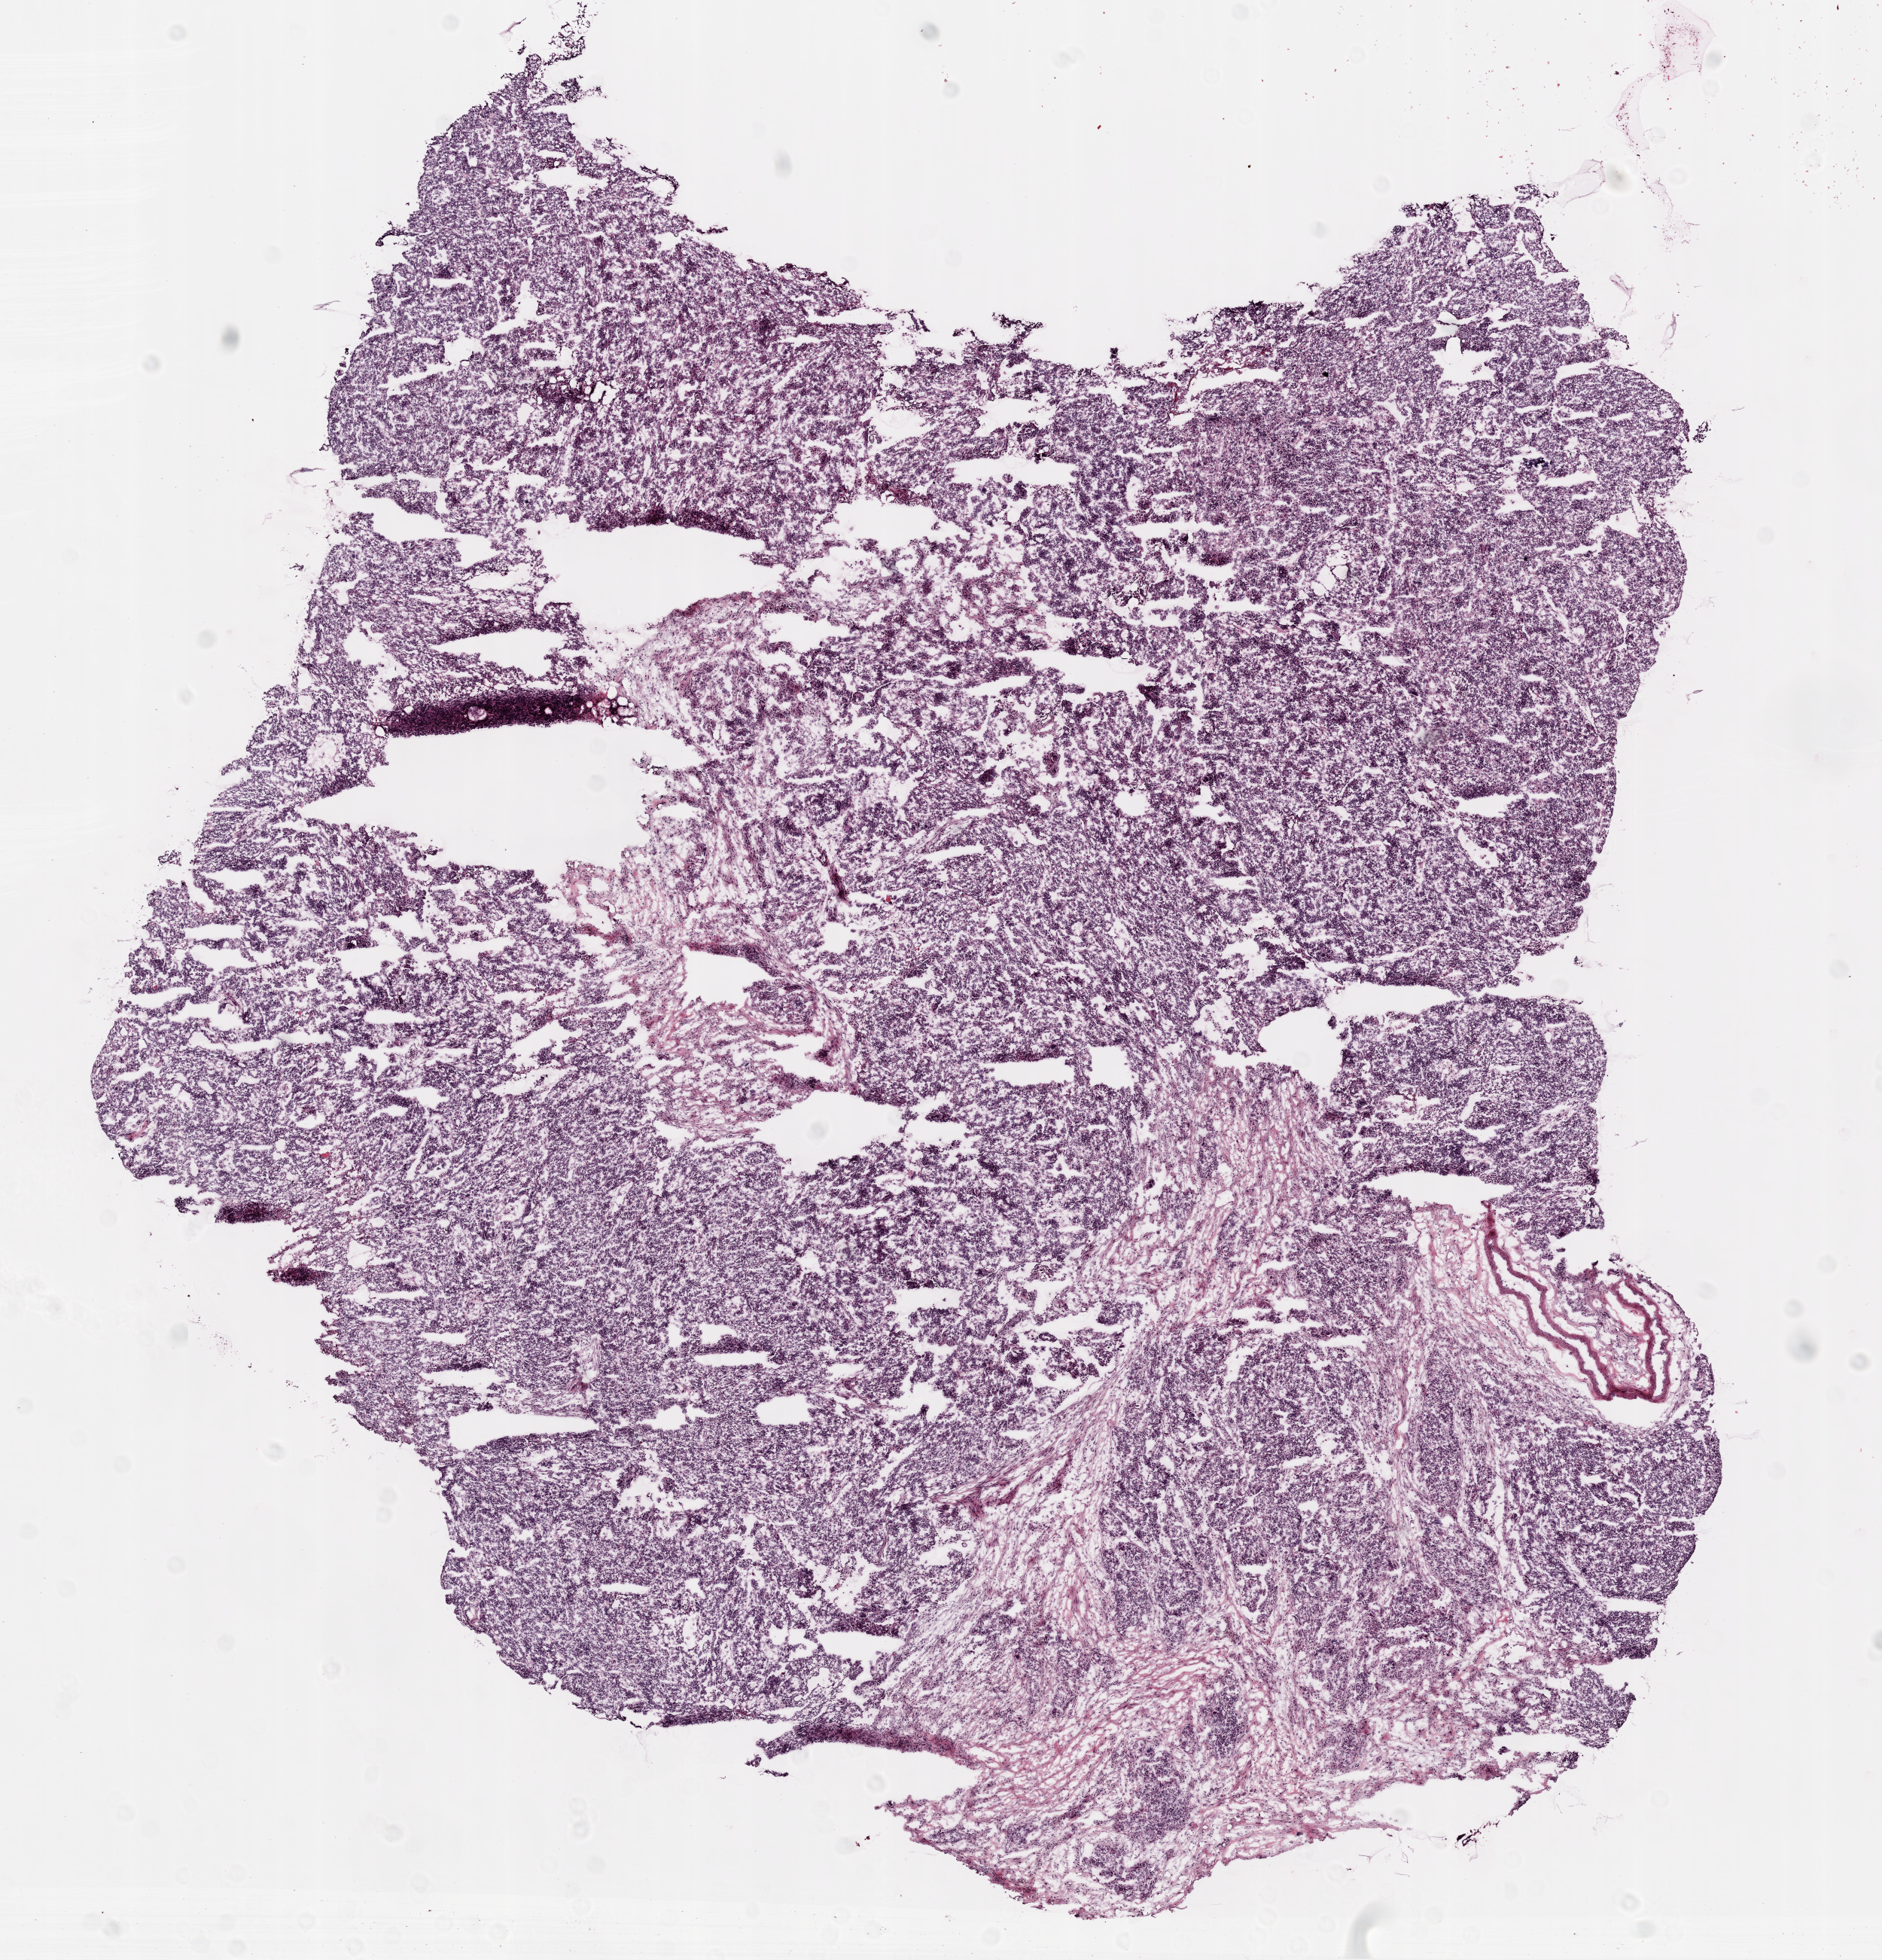
Digitized H&E-stained tissue section (whole slide) — low-resolution overview of the scanned area, about 10.0 x 10.4 mm (from a 20x scan). Frozen section from the top of the tissue portion. Sample: primary tumour, ovary. Female, age 55 years at initial diagnosis. Histologic grade: G3 (poorly differentiated). Slide review estimates, as recorded: tumour cells 88%, tumour nuclei 70%, normal cells 0%, stromal cells 10%, necrosis 2%. Infiltration values recorded for this section: lymphocyte infiltration 15%.
Pathologic diagnosis: Serous cystadenocarcinoma, NOS. Laterality: right. FIGO stage: IIIC.